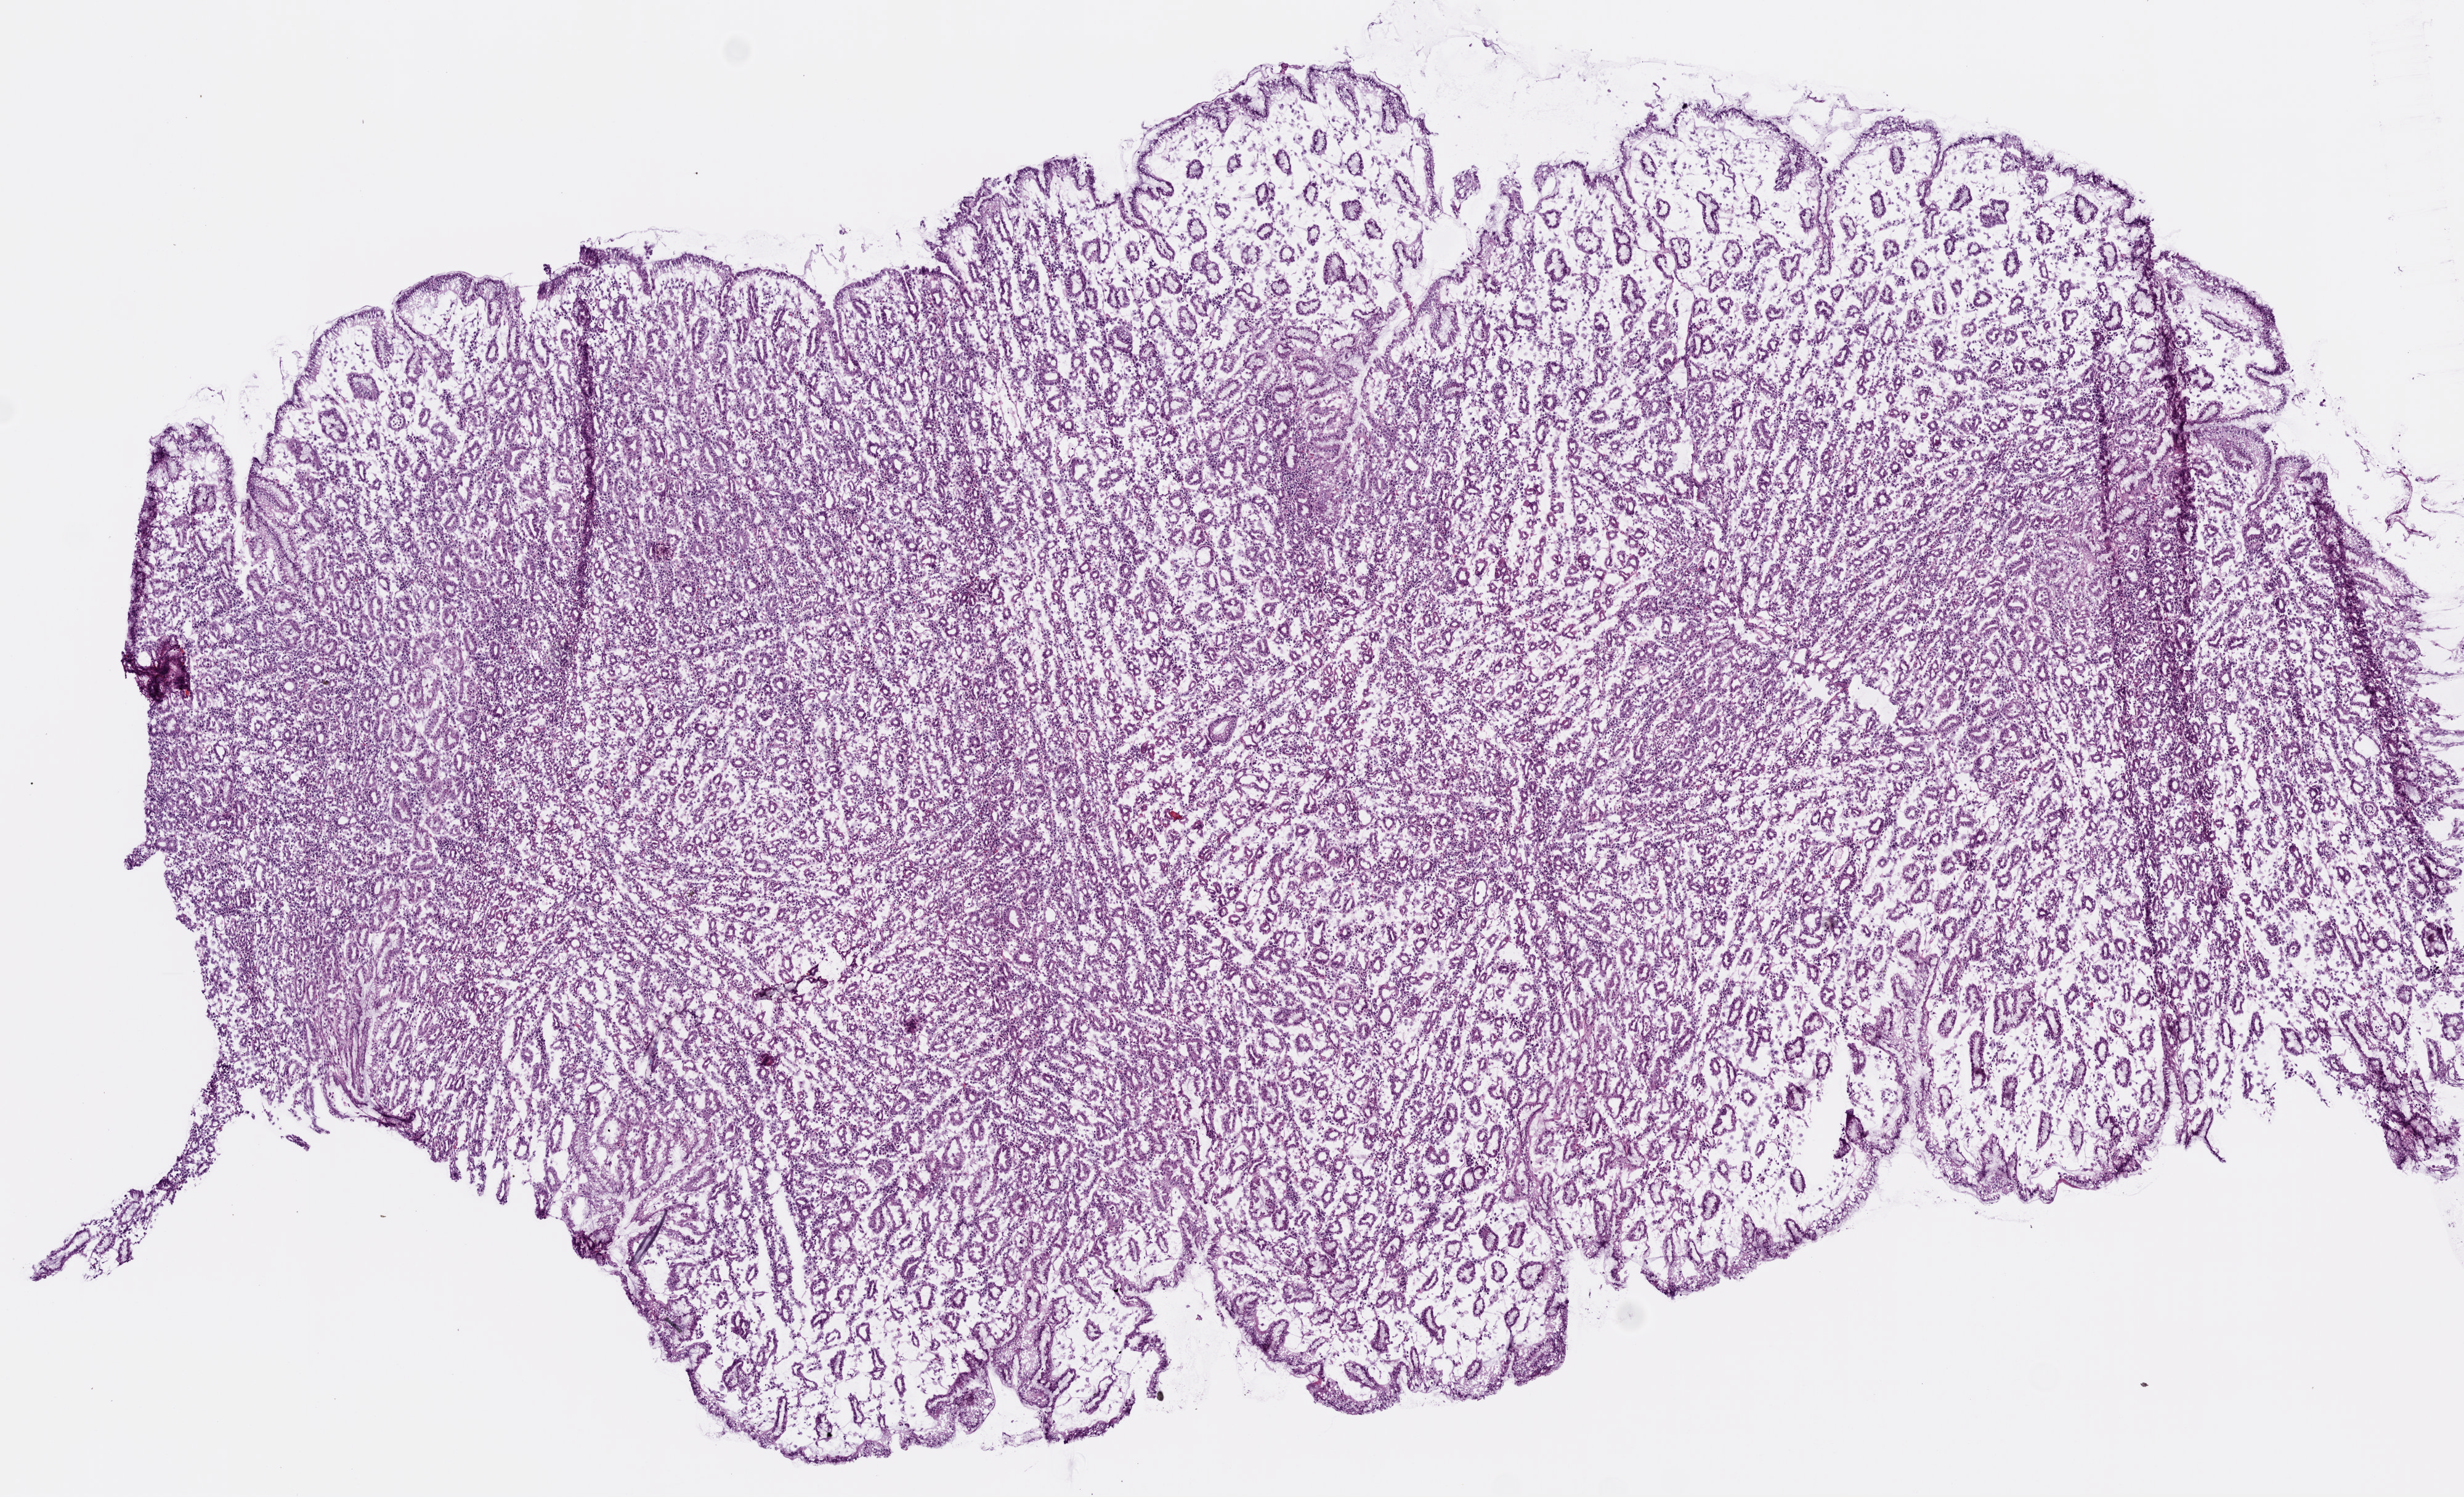
Digitized H&E tissue section (whole slide) — a low-resolution overview of the entire scanned area, about 8.0 x 4.9 mm (from a 20x scan), frozen section, solid tissue normal (non-tumour tissue) sample from the stomach. Patient: male, age at initial diagnosis 59 years.
This section: solid tissue normal (non-tumour) sample from the same patient. Patient diagnosis: Carcinoma, diffuse type.